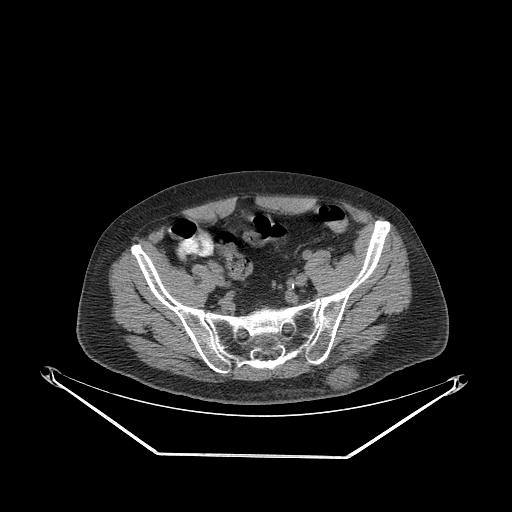
CT of an extremity soft-tissue mass (from a PET/CT study), one axial slice; slice 73 of 267 in the series (ordered by position); reconstruction kernel STANDARD; soft-tissue window (W 400 / L 40 HU); 3.75 mm slice thickness; 512 × 512 image matrix. Male patient. From the clinical record (not read from this slice): histological type: leiomyosarcoma; grade: intermediate; site of the primary tumour: left pelvis.
Structures marked on this image (expert contour drawn on MRI and transferred to this co-registered scan by the dataset authors):
- gross tumour volume (mass): bounding box <333,368,355,389> (left, top, right, bottom; pixels)